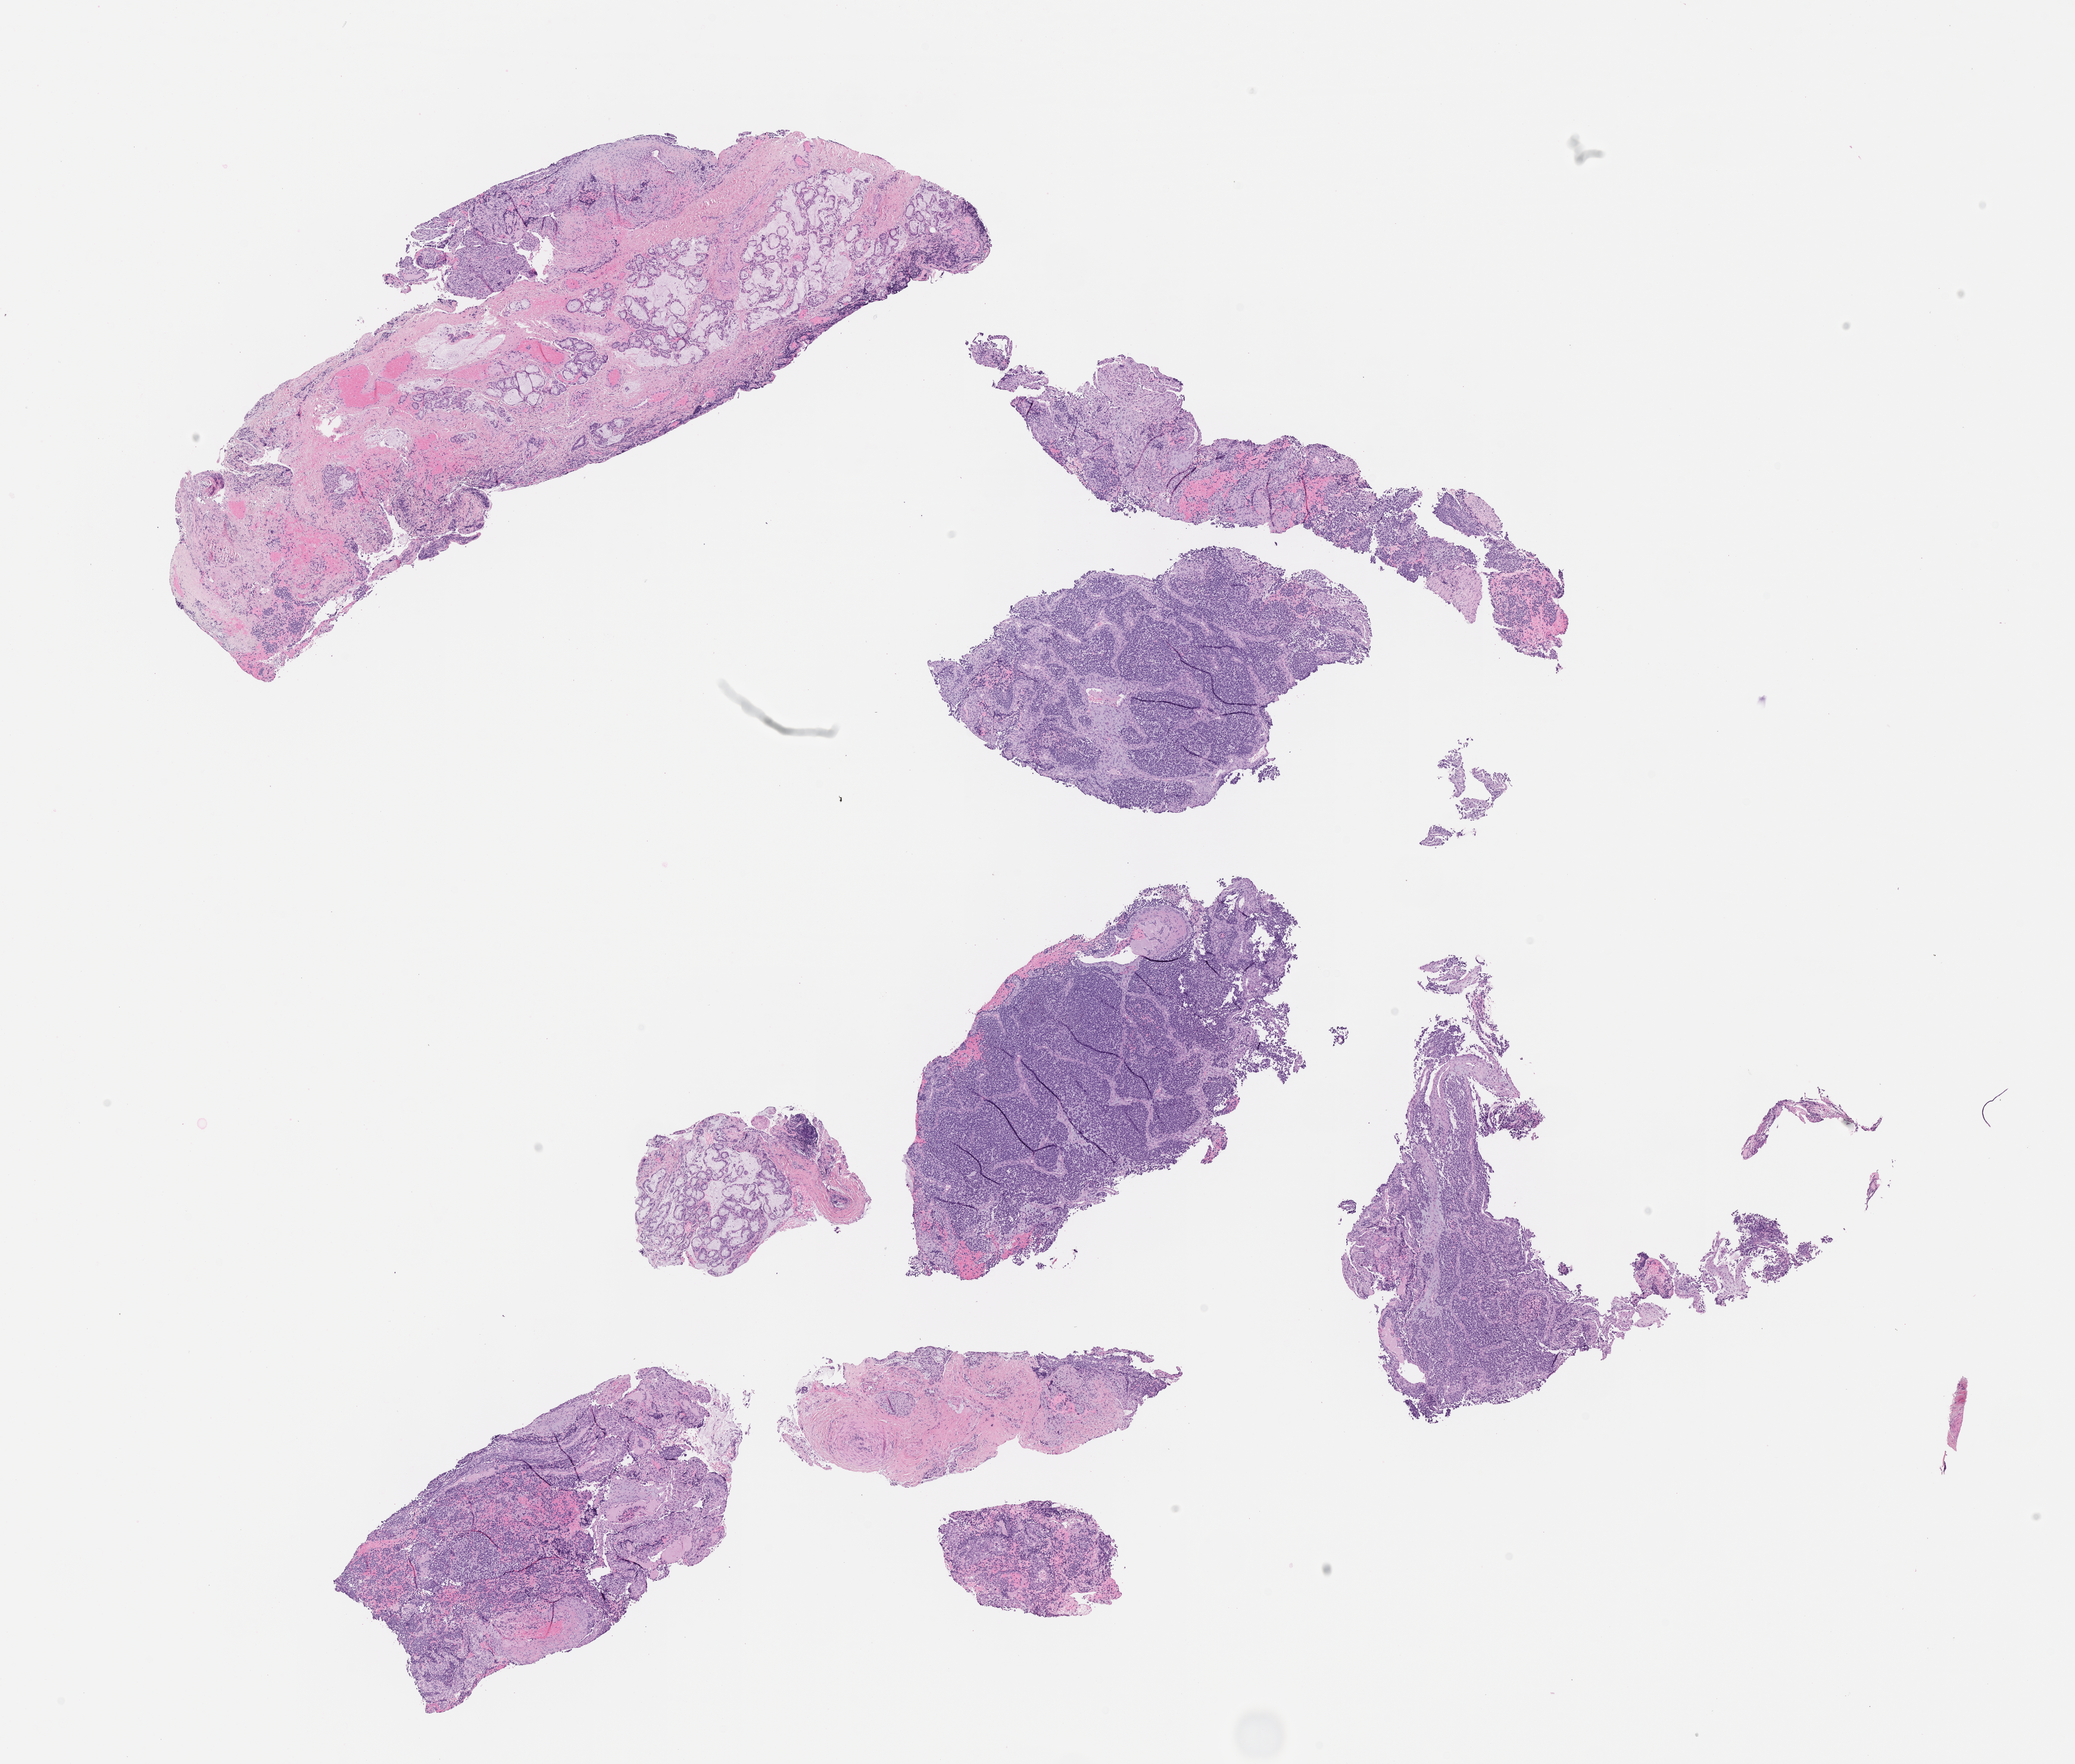
Hematoxylin and eosin (H&E) whole-slide image of tumor tissue, a low-resolution overview of the entire scanned area, about 14.1 x 12.0 mm; FFPE section; site: nasal cavity. Male patient, age at diagnosis 2.2 years.
* stage (as recorded): 4
* metastatic status at presentation (as recorded): metastatic (confirmed)
* diagnosis: rhabdomyosarcoma; histological classification: alveolar rhabdomyosarcoma